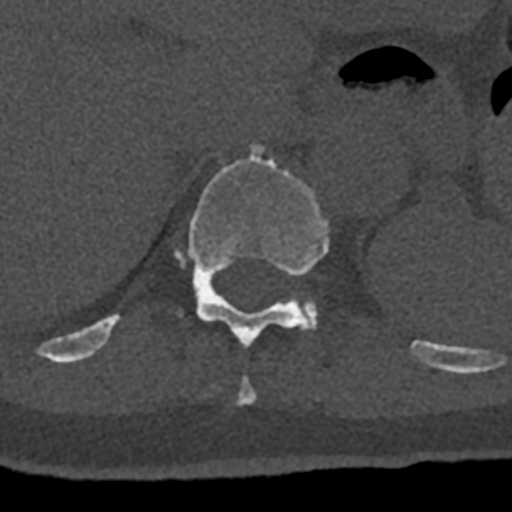
CT including the spine, one axial slice; reconstruction kernel Br40s/3; bone window (W 1800 / L 400 HU); 0.5 mm slice thickness; 512 × 512 image matrix. Male patient, age 74 years. From the clinical record (not read from this slice): primary cancer: renal.
Annotated regions visible in this slice (semi-automatic segmentation, software-assisted and operator-edited):
- T10 vertebra: bounding box <236,376,257,405> (left, top, right, bottom; pixels)
- T11 vertebra: <70,144,432,366>
- T12 vertebra: <303,300,317,329>